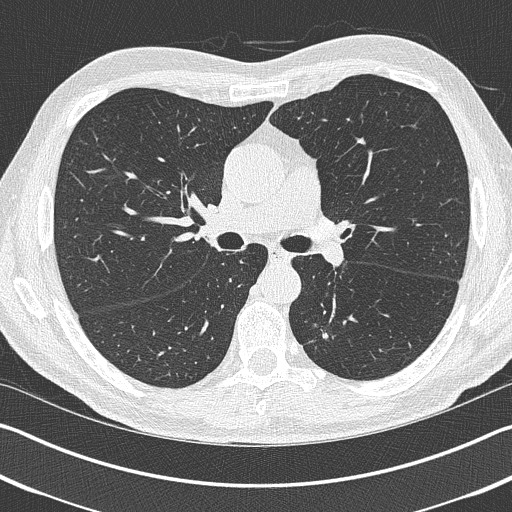
Low-dose screening chest CT, axial slice, baseline screening round, lung window (W 1500 / L -600 HU), 1 mm slice thickness, 120 kVp, 512 × 512 image matrix. Male participant, aged 69 years at enrolment. Current smoker at enrolment.
Expert reader's lesion annotation, bounding box <303,310,357,360> (left, top, right, bottom; pixels). Reader record for this screening exam (exam-level; its link to the box is not recorded): non-calcified nodule or mass ≥4 mm, left upper lobe, 19 × 19 mm, spiculated (stellate) margins, pre-existing on the prior screen: yes. Official screen result: positive, change unspecified: nodule(s) >= 4 mm or enlarging nodule(s), mass(es), or other non-specific abnormalities suspicious for lung cancer.